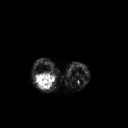
FDG PET of an extremity soft-tissue mass (from a PET/CT study), one axial slice; slice 175 of 267 in the series (ordered by position); 3.27 mm slice thickness; 128 × 128 image matrix, field of view 500 × 500 mm. Patient: female, 62 years. From the clinical record (not read from this slice): histological type: liposarcoma; site of the primary tumour: right thigh.
Outlined on this slice (expert contour drawn on MRI and transferred to this co-registered scan by the dataset authors):
- gross tumour volume (mass): box from (x=35, y=72) to (x=56, y=90) px